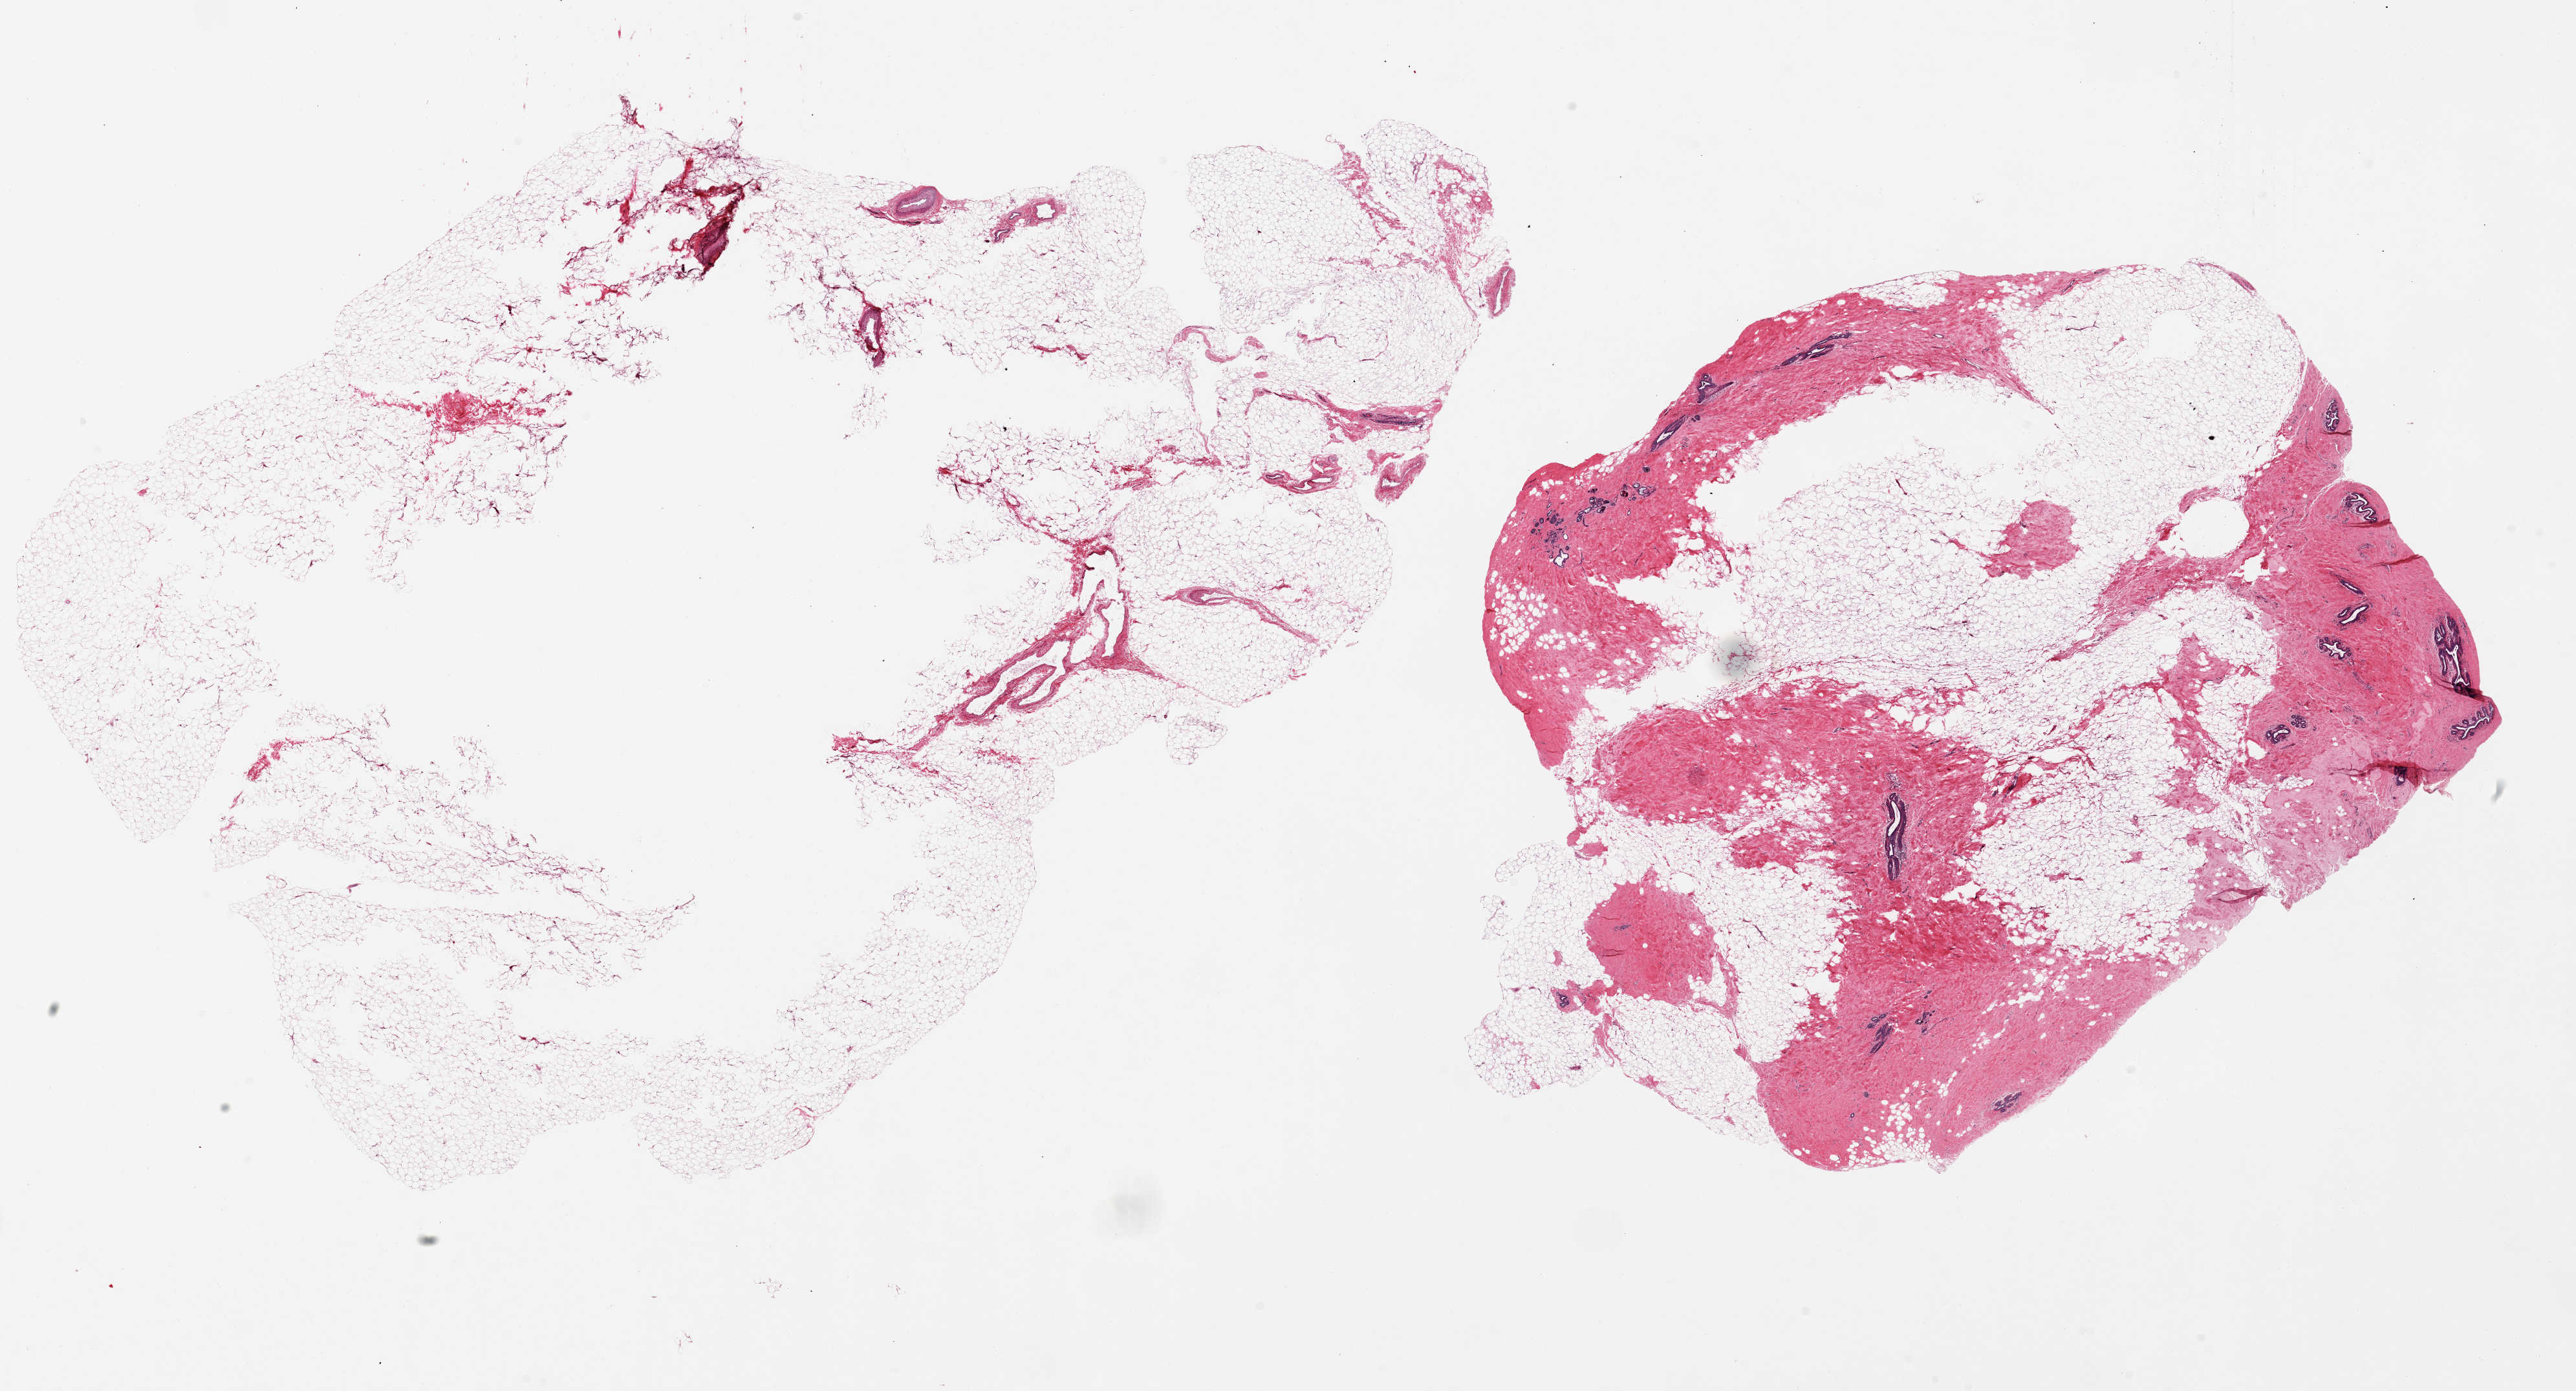
Digitized H&E-stained section — low-resolution overview of the scanned area, about 31.5 x 17.0 mm. PAXgene-fixed paraffin-embedded (PFPE) section. Sampled site (target tissue): breast. Donor tissue sample. Donor: female.
Reviewer comment on this tissue sample: 2 pieces, 18x11 & 14x10mm; ~20% with gynecomastoid ductal/stromal hyperplasia.